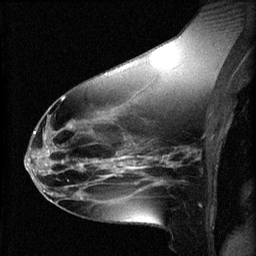
Breast MRI (dynamic contrast-enhanced), one sagittal slice; position 30 of 60 along the scan axis; 3 images stored at this slice position (order not interpretable as contrast timing); 1.5 T; TE 4.2 ms, TR 8.2 ms; 2 mm slice thickness; 256 × 256 image matrix. Female patient, age 49 years.
Structures marked on this image (semi-automatically segmented with operator editing):
- analysis volume of interest (the breast-tissue region the enhancement analysis was run in; not a lesion): bounding box (x1, y1, x2, y2) in pixels: (45, 136, 109, 187)
- tumour enhancement mask (voxels above the 70 % enhancement threshold inside the analysis volume of interest): (45, 136, 107, 173)